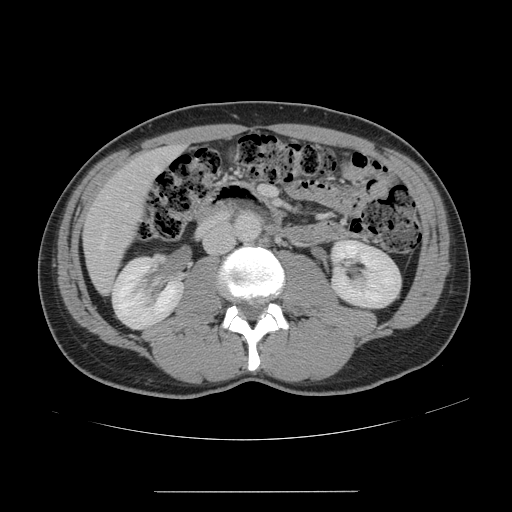
Contrast-enhanced abdominal CT, one axial slice; position 48 of 178 along the scan axis; intravenous contrast given; soft-tissue window (W 400 / L 40 HU); 2.5 mm slice thickness; 512 × 512 image matrix, field of view 401 × 401 mm. Male patient, age 53 years. From the clinical record (not read from this slice): diagnosis: colorectal cancer liver metastases, imaged before liver resection; multiple liver metastases: yes; largest metastasis: 2.4 cm; disease in both lobes: no.
Structures marked on this image (outlined manually by an expert reader):
- hepatic veins: bounding box [x1, y1, x2, y2] px = [99, 167, 159, 250]
- liver: [84, 148, 178, 293]
- portal vein (with intrahepatic branches): [260, 188, 267, 195]